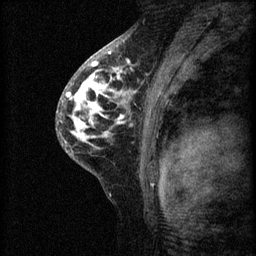
Breast MRI (dynamic contrast-enhanced), one sagittal slice. Slice 41 of 60 in the series (ordered by position). 3 images stored at this slice position (order not interpretable as contrast timing). 1.5 T. TE 4.2 ms, TR 8.2 ms. 2 mm slice thickness. 256 × 256 image matrix, field of view 180 × 180 mm. Female patient, age 41 years.
Structures marked on this image (semi-automatically segmented with operator editing):
- analysis volume of interest (the breast-tissue region the enhancement analysis was run in; not a lesion): box from (x=56, y=62) to (x=160, y=175) px
- tumour enhancement mask (voxels above the 70 % enhancement threshold inside the analysis volume of interest): (x=60, y=62)–(x=136, y=147)